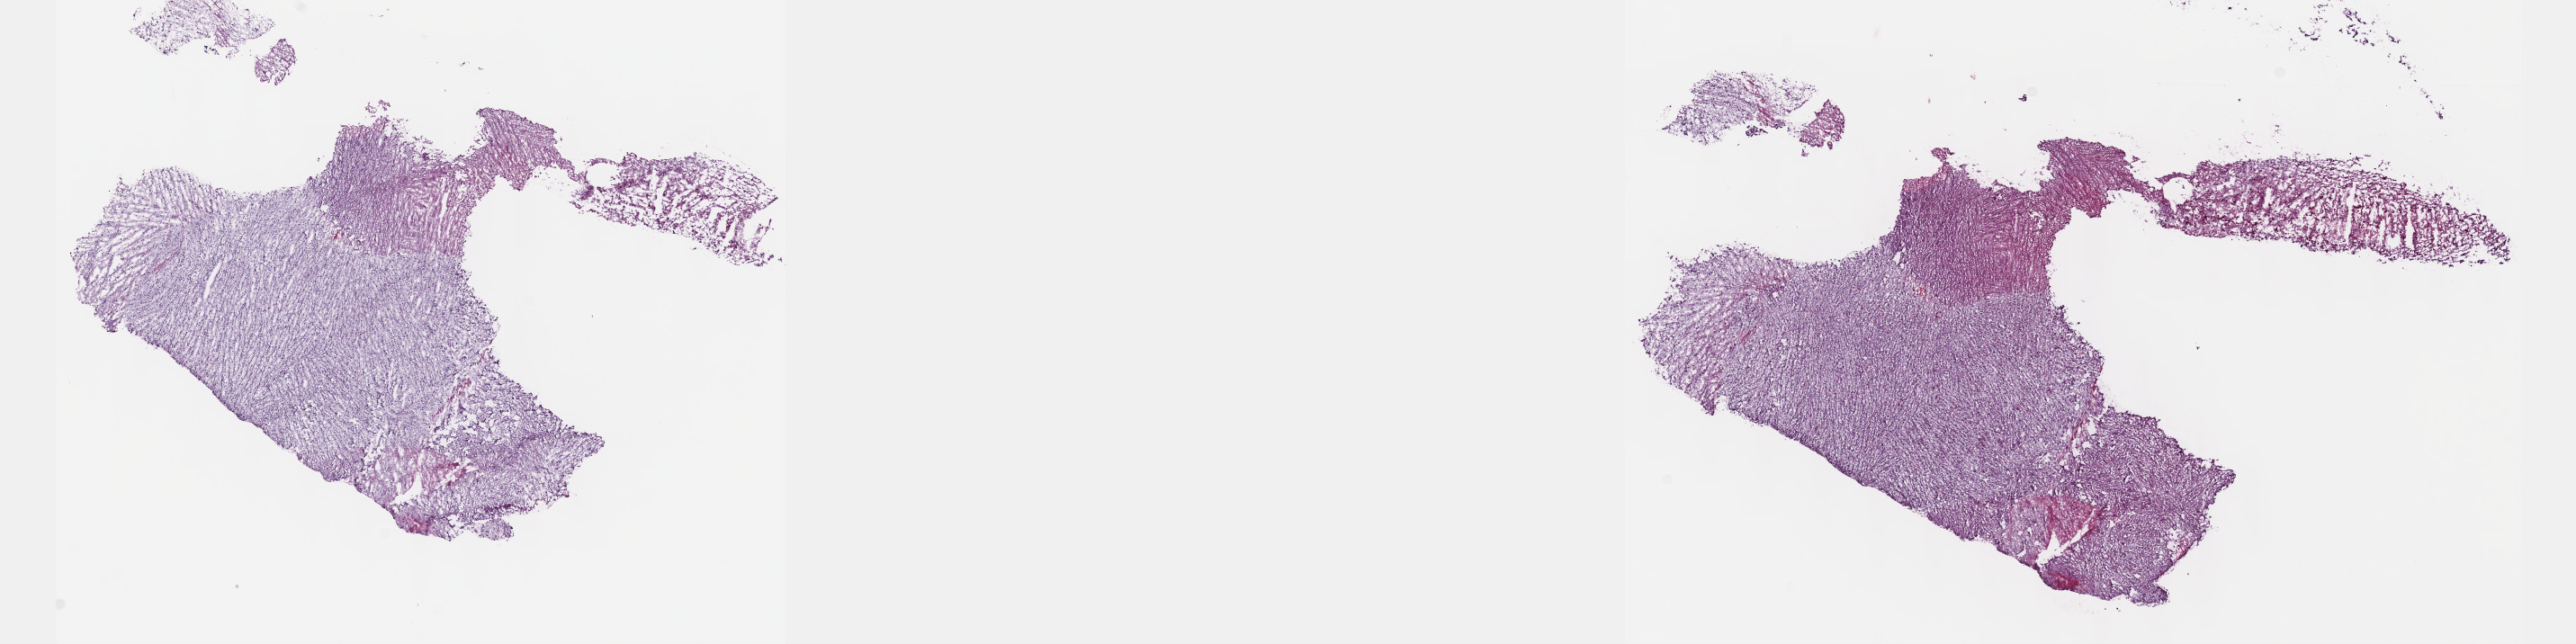
H&E-stained whole-slide image — shown as a low-resolution overview of the whole scanned area (about 23.1 x 5.8 mm), frozen section from the top of the tissue portion, brain, primary tumour sample. Male, age 56 years at initial diagnosis. Histologic grade: G2 (moderately differentiated). Composition of this section per pathologist review: tumour cells 50%, tumour nuclei 80%, normal cells 20%, stromal cells 30%, necrosis 0%. Inflammatory infiltration, as recorded: lymphocyte infiltration 0%, monocyte infiltration 0%, neutrophil infiltration 0%.
Histologic diagnosis: Oligodendroglioma, NOS (cerebrum). Laterality: right.